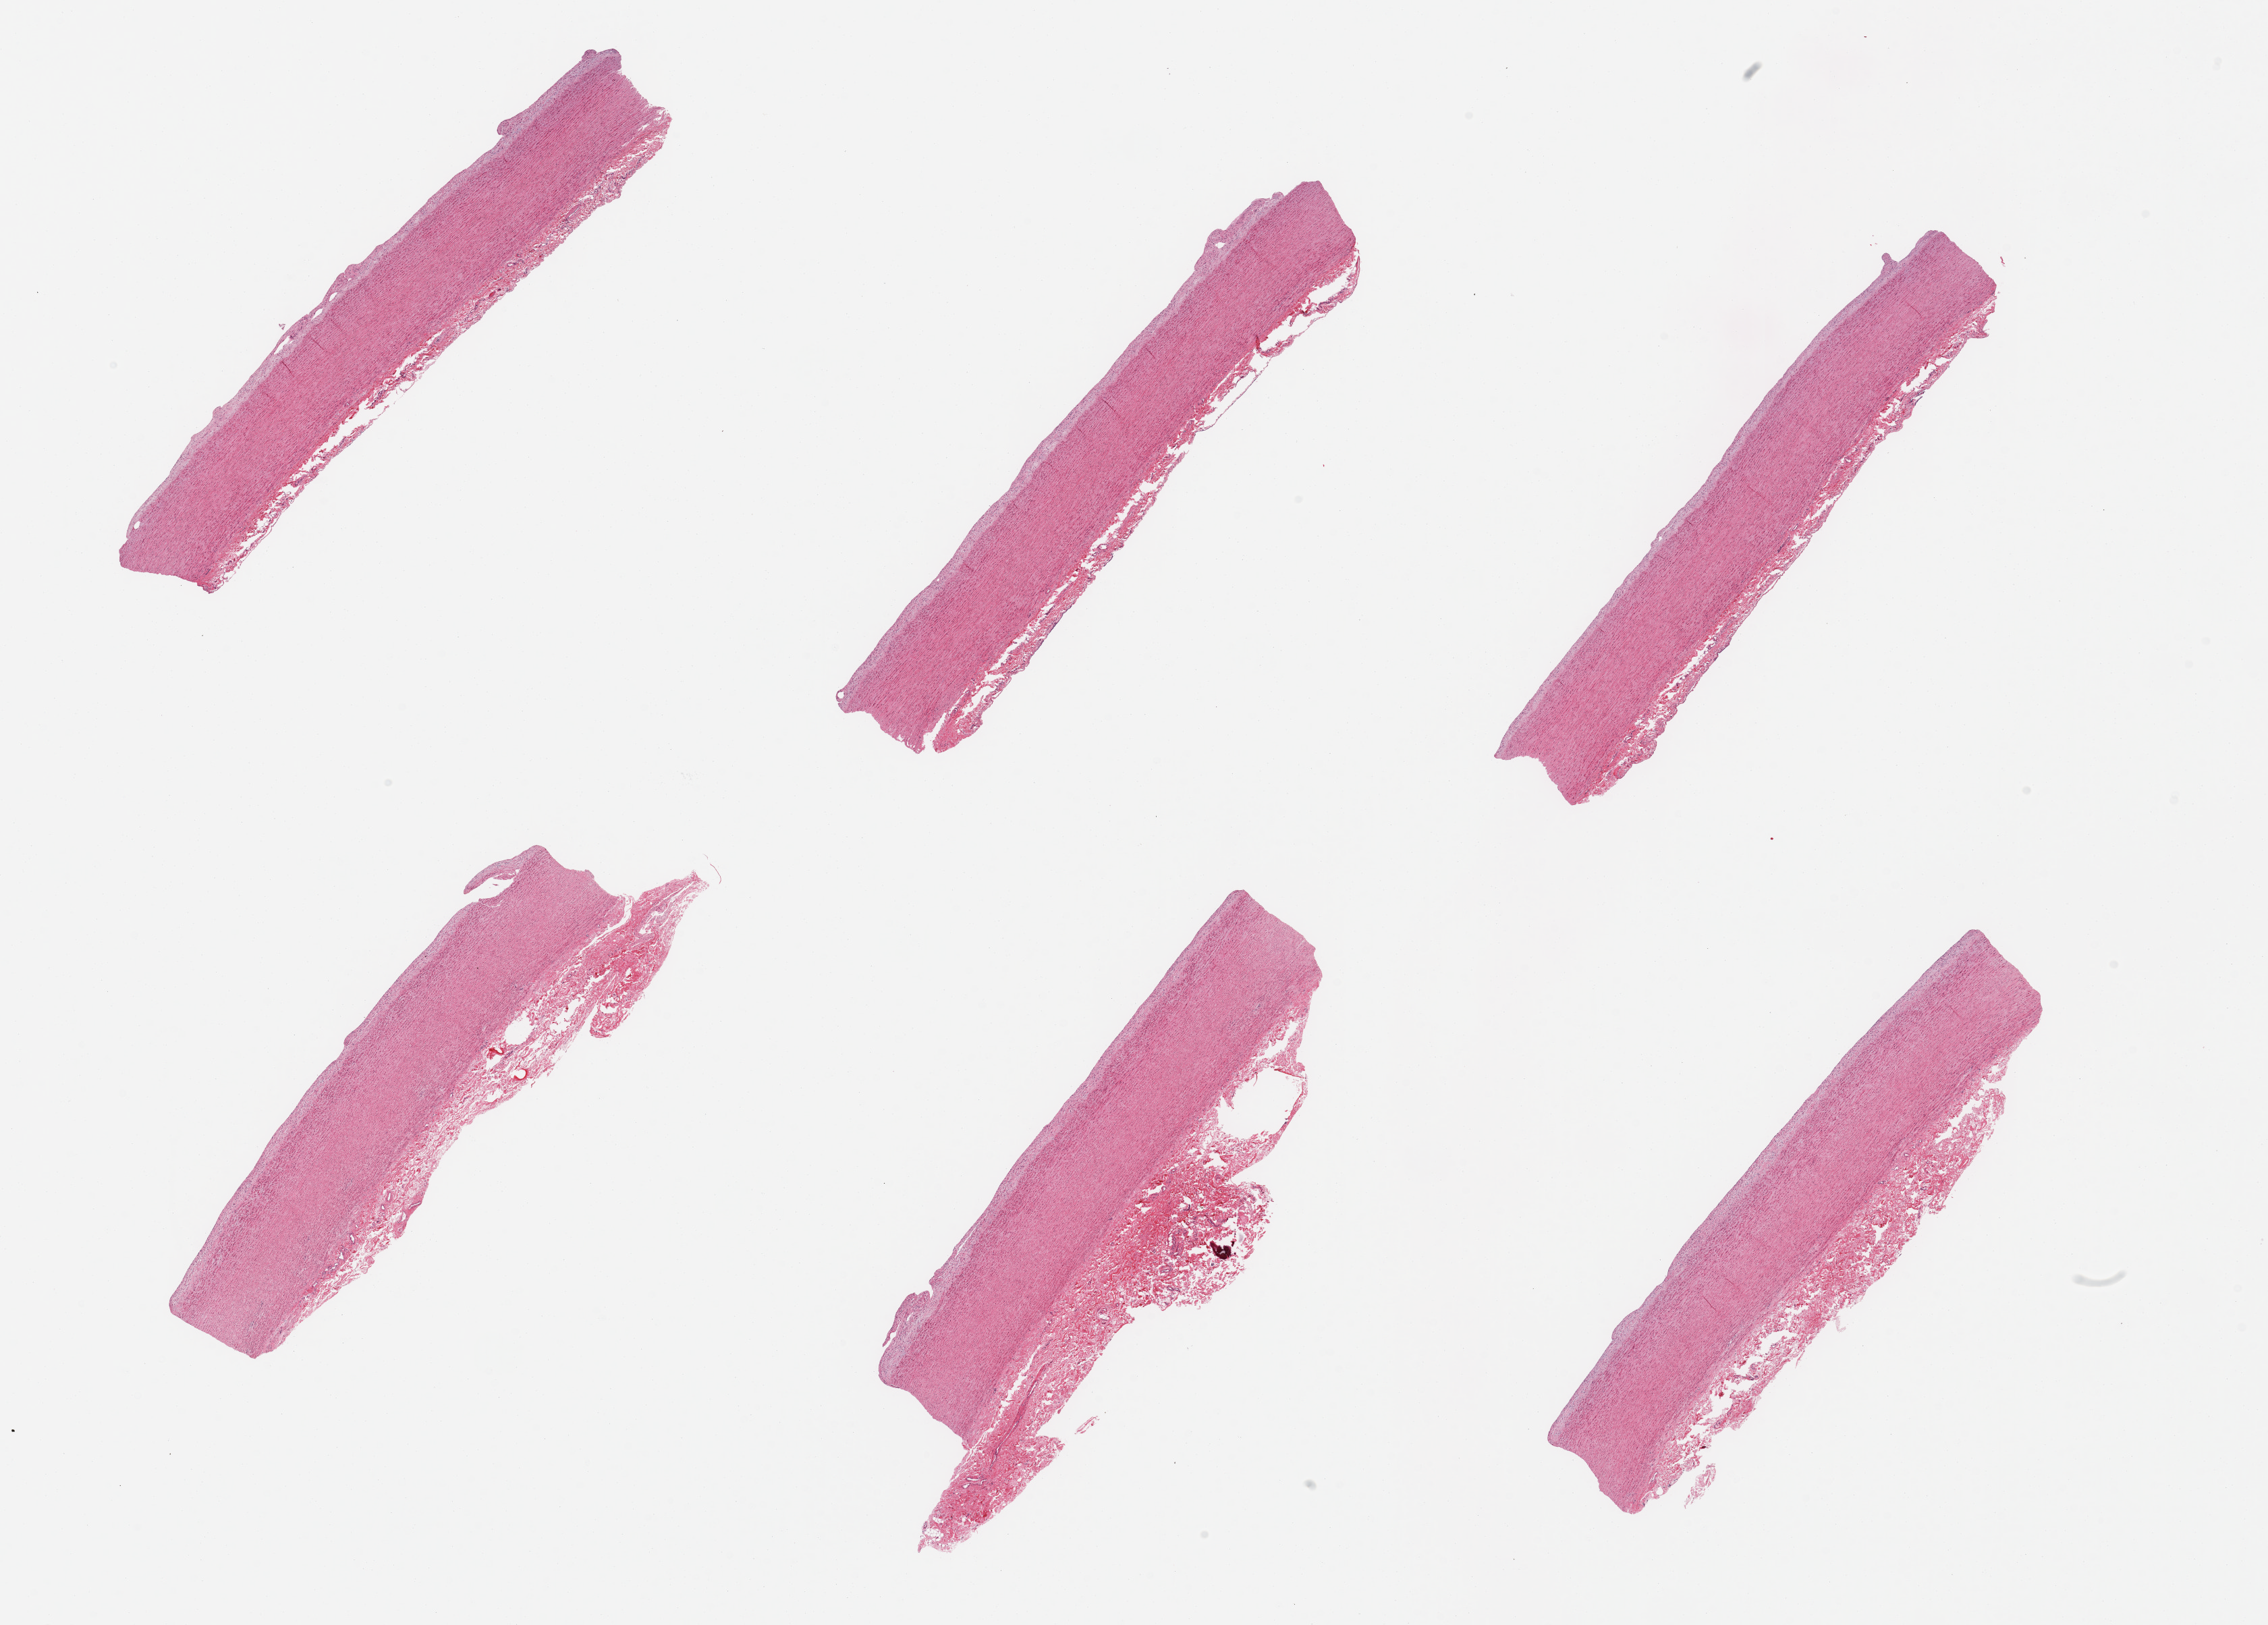
Digitized H&E-stained section — whole scanned area (about 26.6 x 19.0 mm, from a 20x scan) shown as a low-resolution overview, PAXgene-fixed, paraffin-embedded tissue, target tissue: aorta, tissue donor sample. Donor sex: female.
Reviewer comment on this tissue sample: 6 pieces; mild plaque formation.